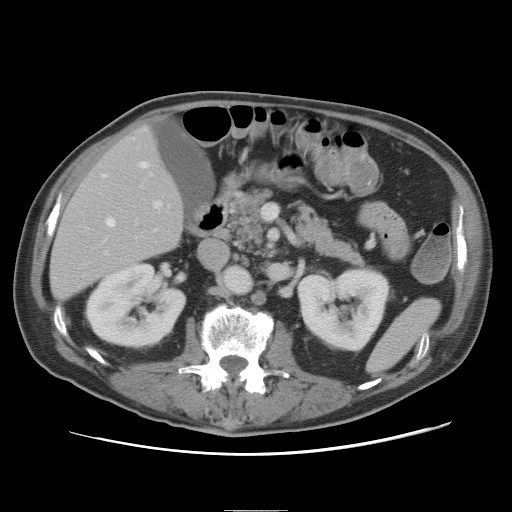
Contrast-enhanced abdominal CT, one axial slice; slice 31 of 89 in the series (ordered by position); 120 kVp; intravenous contrast given; soft-tissue window (W 400 / L 40 HU); 512 × 512 image matrix, field of view 375 × 375 mm. Male patient, age 69 years. Case-level facts recorded for this patient, not image findings: diagnosis: colorectal cancer liver metastases, imaged before liver resection; multiple liver metastases: no; largest metastasis: 8.5 cm; disease in both lobes: no.
Structures marked on this image (expert manual segmentation):
- hepatic veins: bounding box <103,161,148,227> (left, top, right, bottom; pixels)
- liver: <51,126,182,300>
- planned liver remnant (the part of the liver to remain after resection): <51,126,183,300>
- portal vein (with intrahepatic branches): <106,200,162,253>